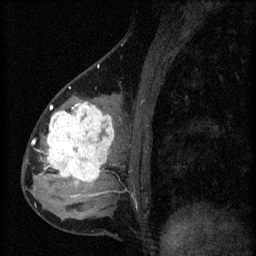
Breast MRI (dynamic contrast-enhanced), one sagittal slice; slice 21 of 60 in the series (ordered by position); 3 images stored at this slice position (order not interpretable as contrast timing); 1.5 T; TE 4.2 ms, TR 8.2 ms; 2 mm slice thickness; 256 × 256 image matrix, field of view 180 × 180 mm. Patient: female, 37 years.
Outlined on this slice (semi-automatic segmentation, software-assisted and operator-edited):
- analysis volume of interest (the breast-tissue region the enhancement analysis was run in; not a lesion): box from (x=44, y=100) to (x=119, y=197) px
- tumour enhancement mask (voxels above the 70 % enhancement threshold inside the analysis volume of interest): (x=46, y=102)–(x=115, y=183)